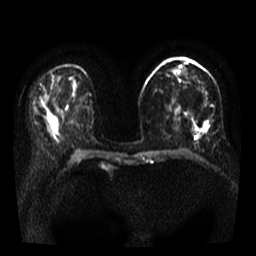
Breast MRI, one axial slice. Diffusion-weighted series; image 2 of 4 stored at this slice position (different b-values; order by instance number). 3 T. 5 mm slice thickness. 256 × 256 image matrix. Female patient.
Outlined on this slice (manually delineated by an expert):
- tumour on diffusion-weighted imaging: bounding box <194,122,209,131> (left, top, right, bottom; pixels)